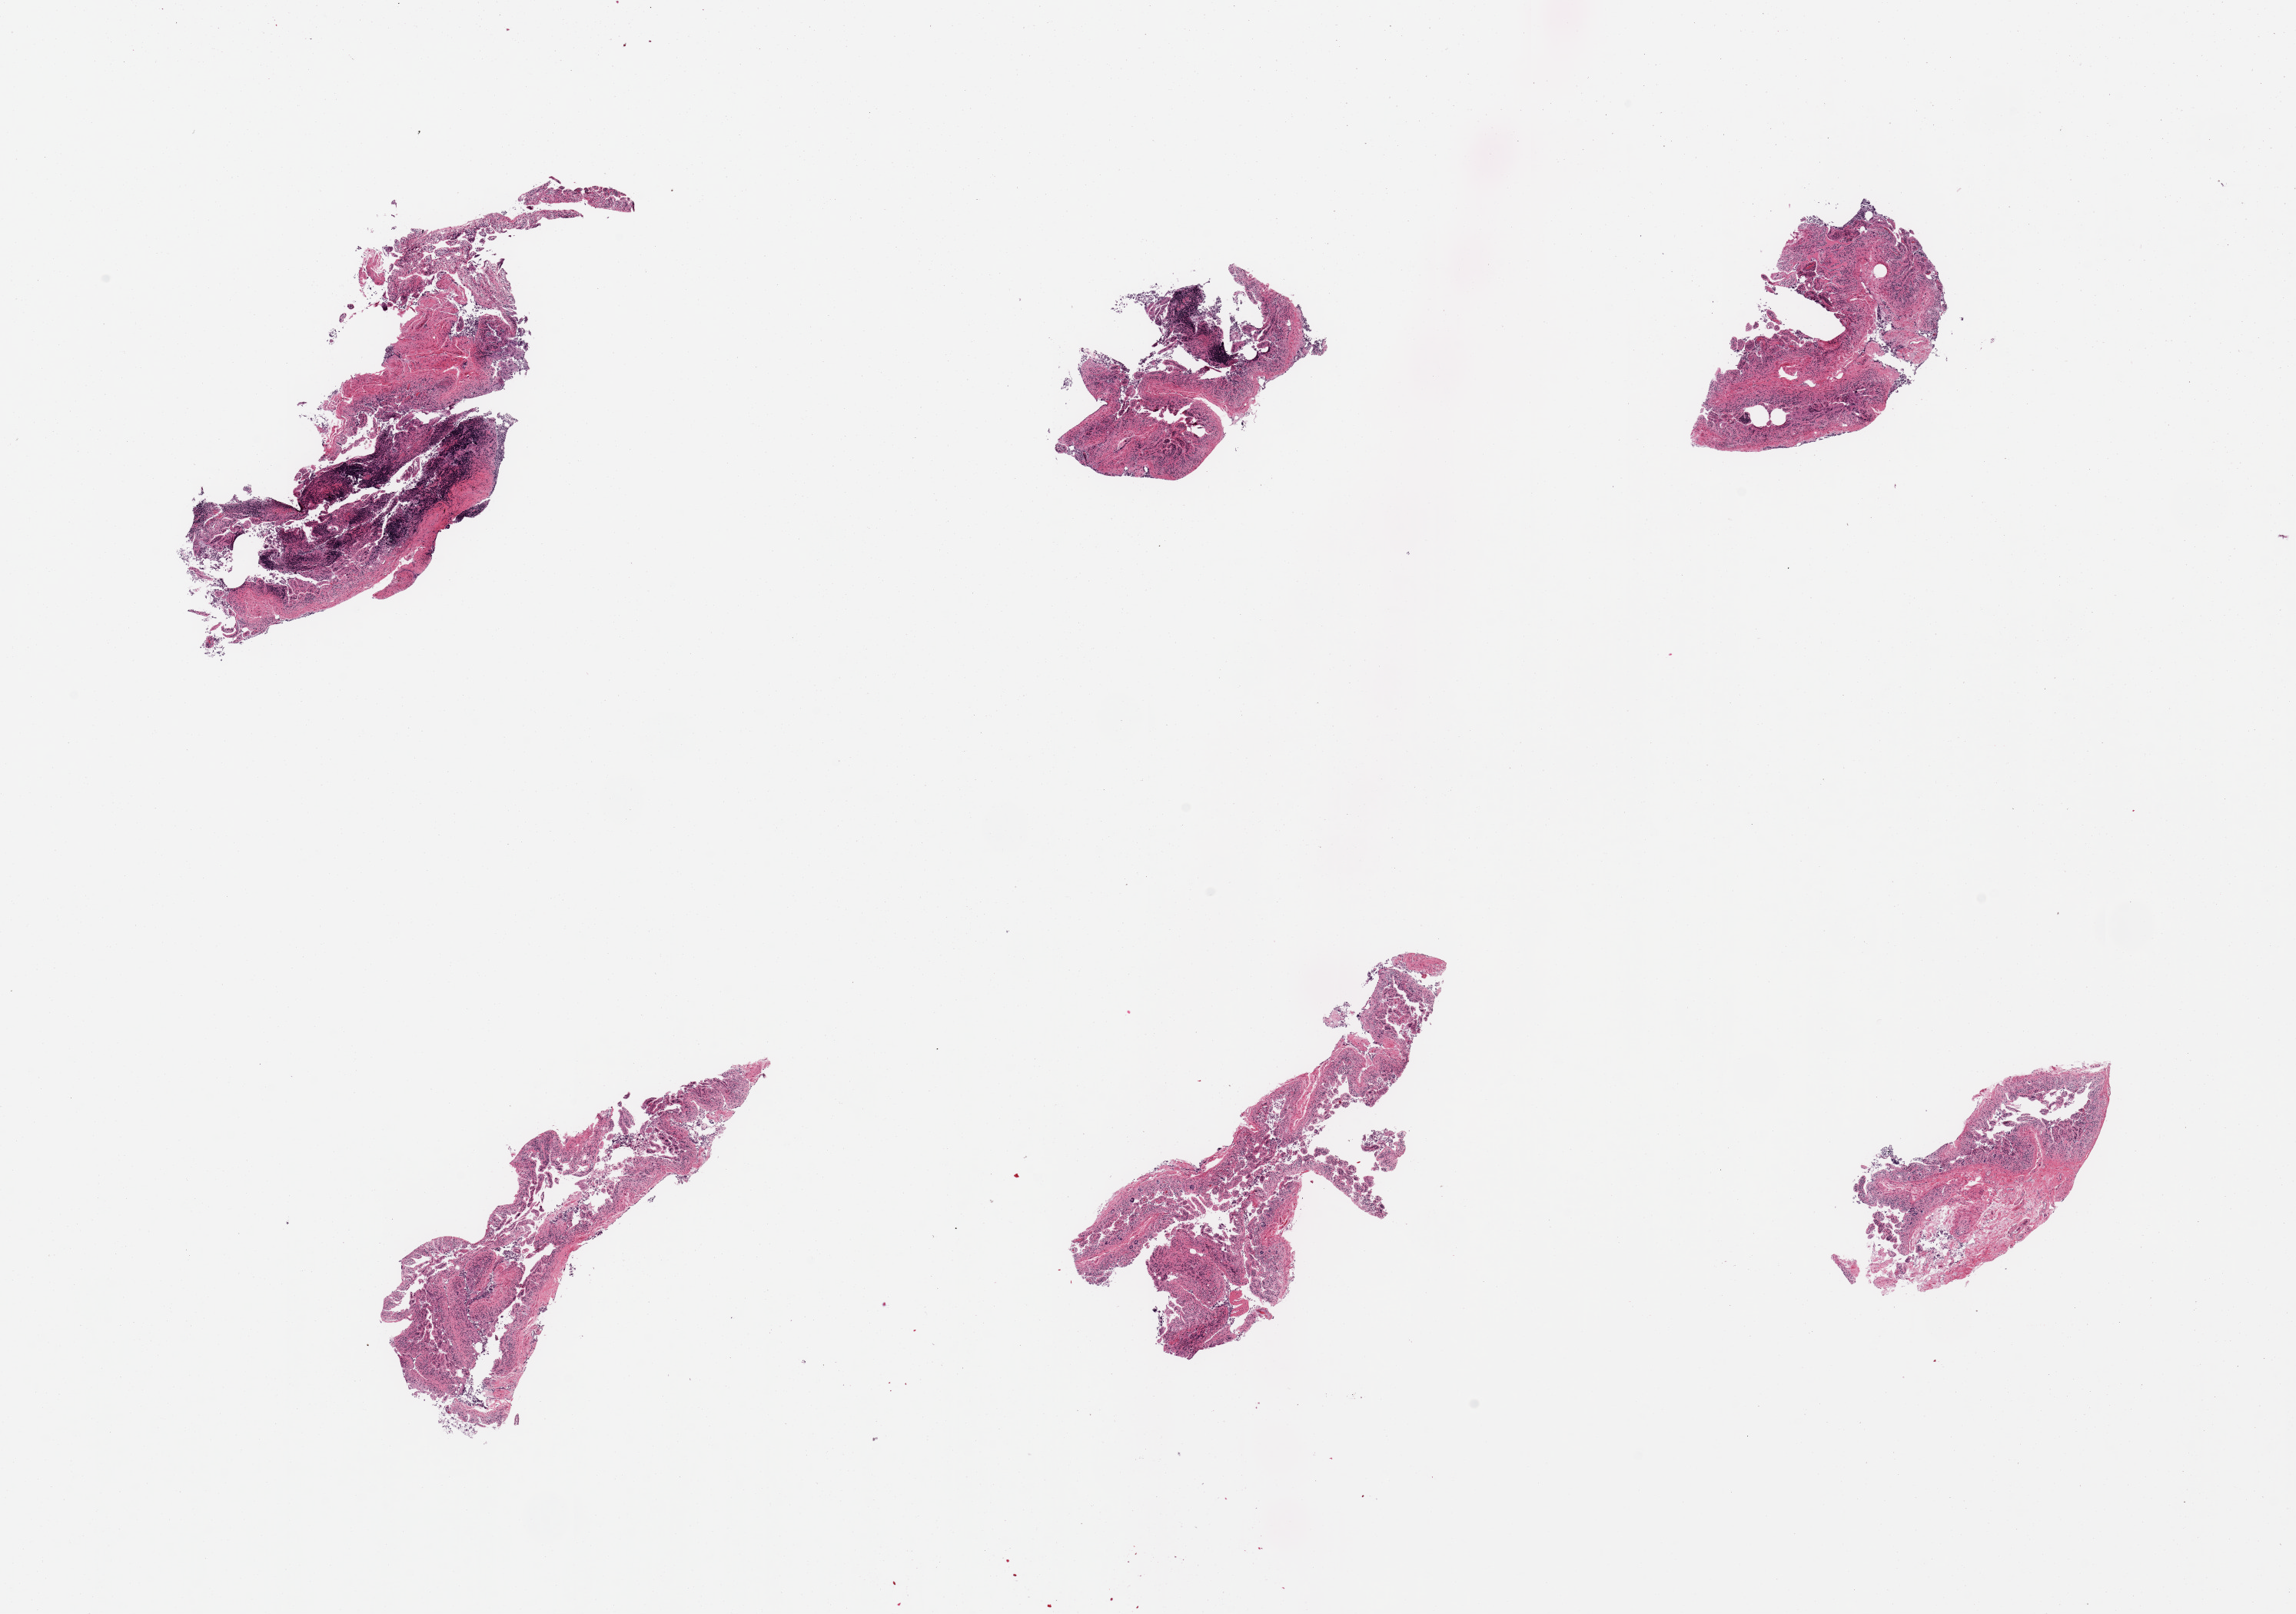
Hematoxylin and eosin (H&E) whole-slide image, brightfield, whole scanned area (about 23.6 x 16.6 mm) shown as a low-resolution overview, PAXgene-fixed paraffin-embedded (PFPE) section, sampled site (target tissue): ileum, tissue donor sample. Donor: male.
Review note (as recorded): 6 pieces; autolyzed mucosa and too few of residual lymphoid aggregates to warrant analysis (<10%).